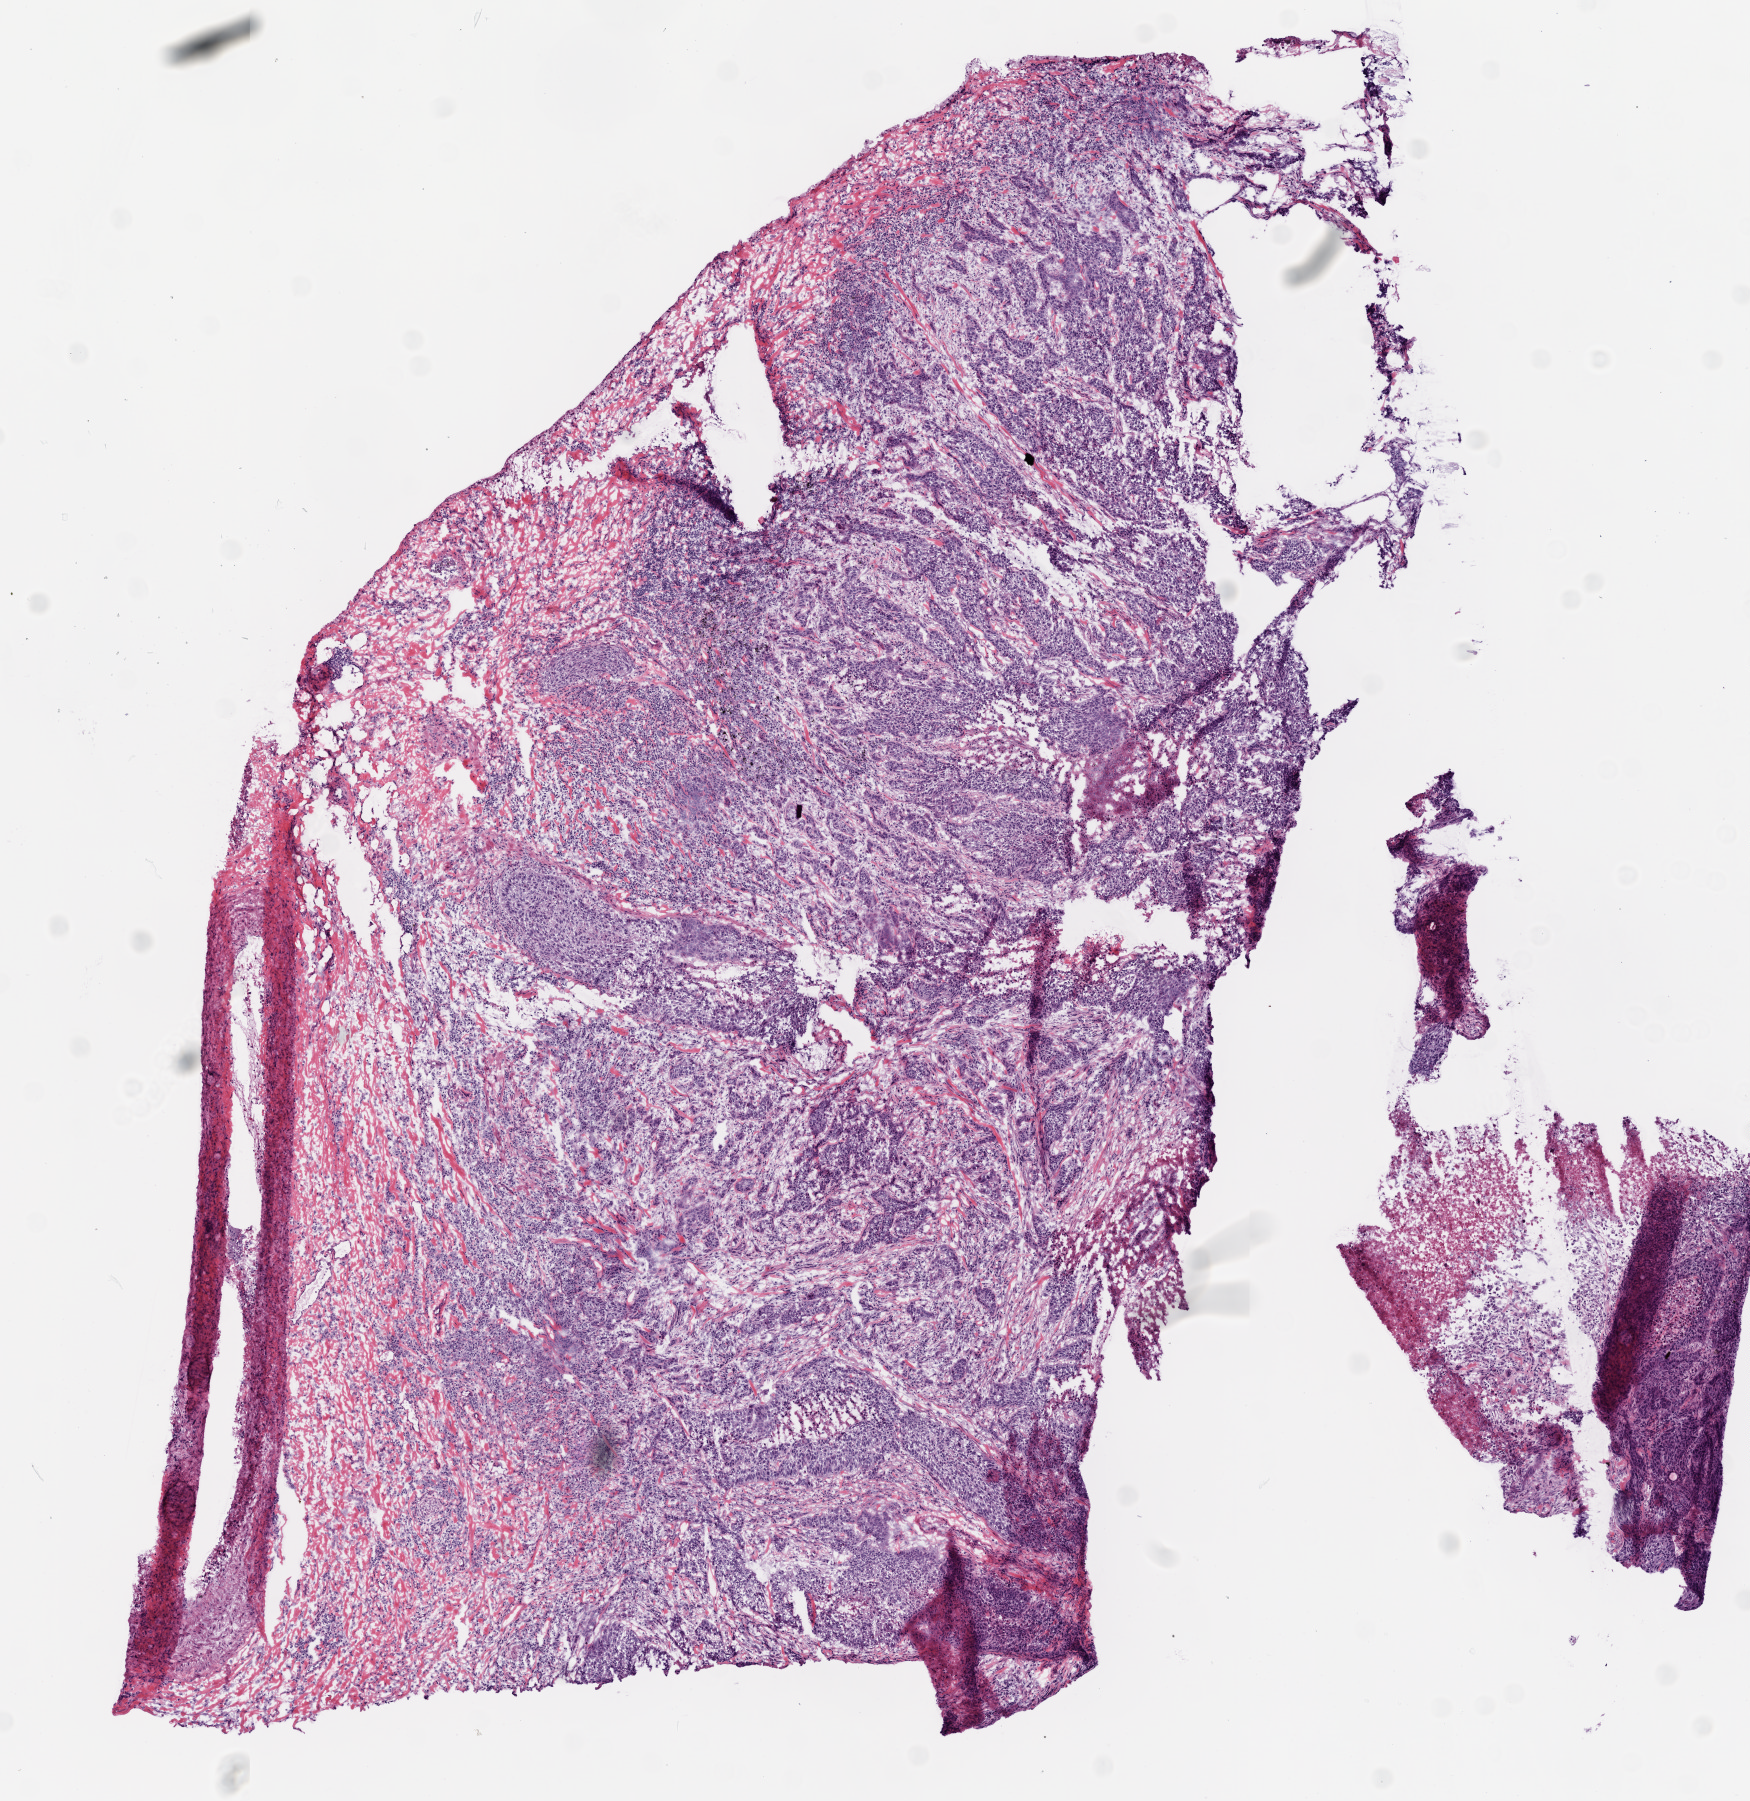
Digitized H&E tissue section (whole slide), shown as a low-resolution overview of the whole scanned area (about 7.0 x 7.2 mm, from a 20x scan), frozen section from the top of the tissue portion, lung, primary tumour sample. Male, age 58 years at initial diagnosis. Composition of this section per pathologist review: tumour cells 82%, tumour nuclei 70%, normal cells 0%, stromal cells 10%, necrosis 8%.
* AJCC pathologic stage: IIB (6th edition)
* histologic diagnosis: Squamous cell carcinoma, NOS (lower lobe, lung)